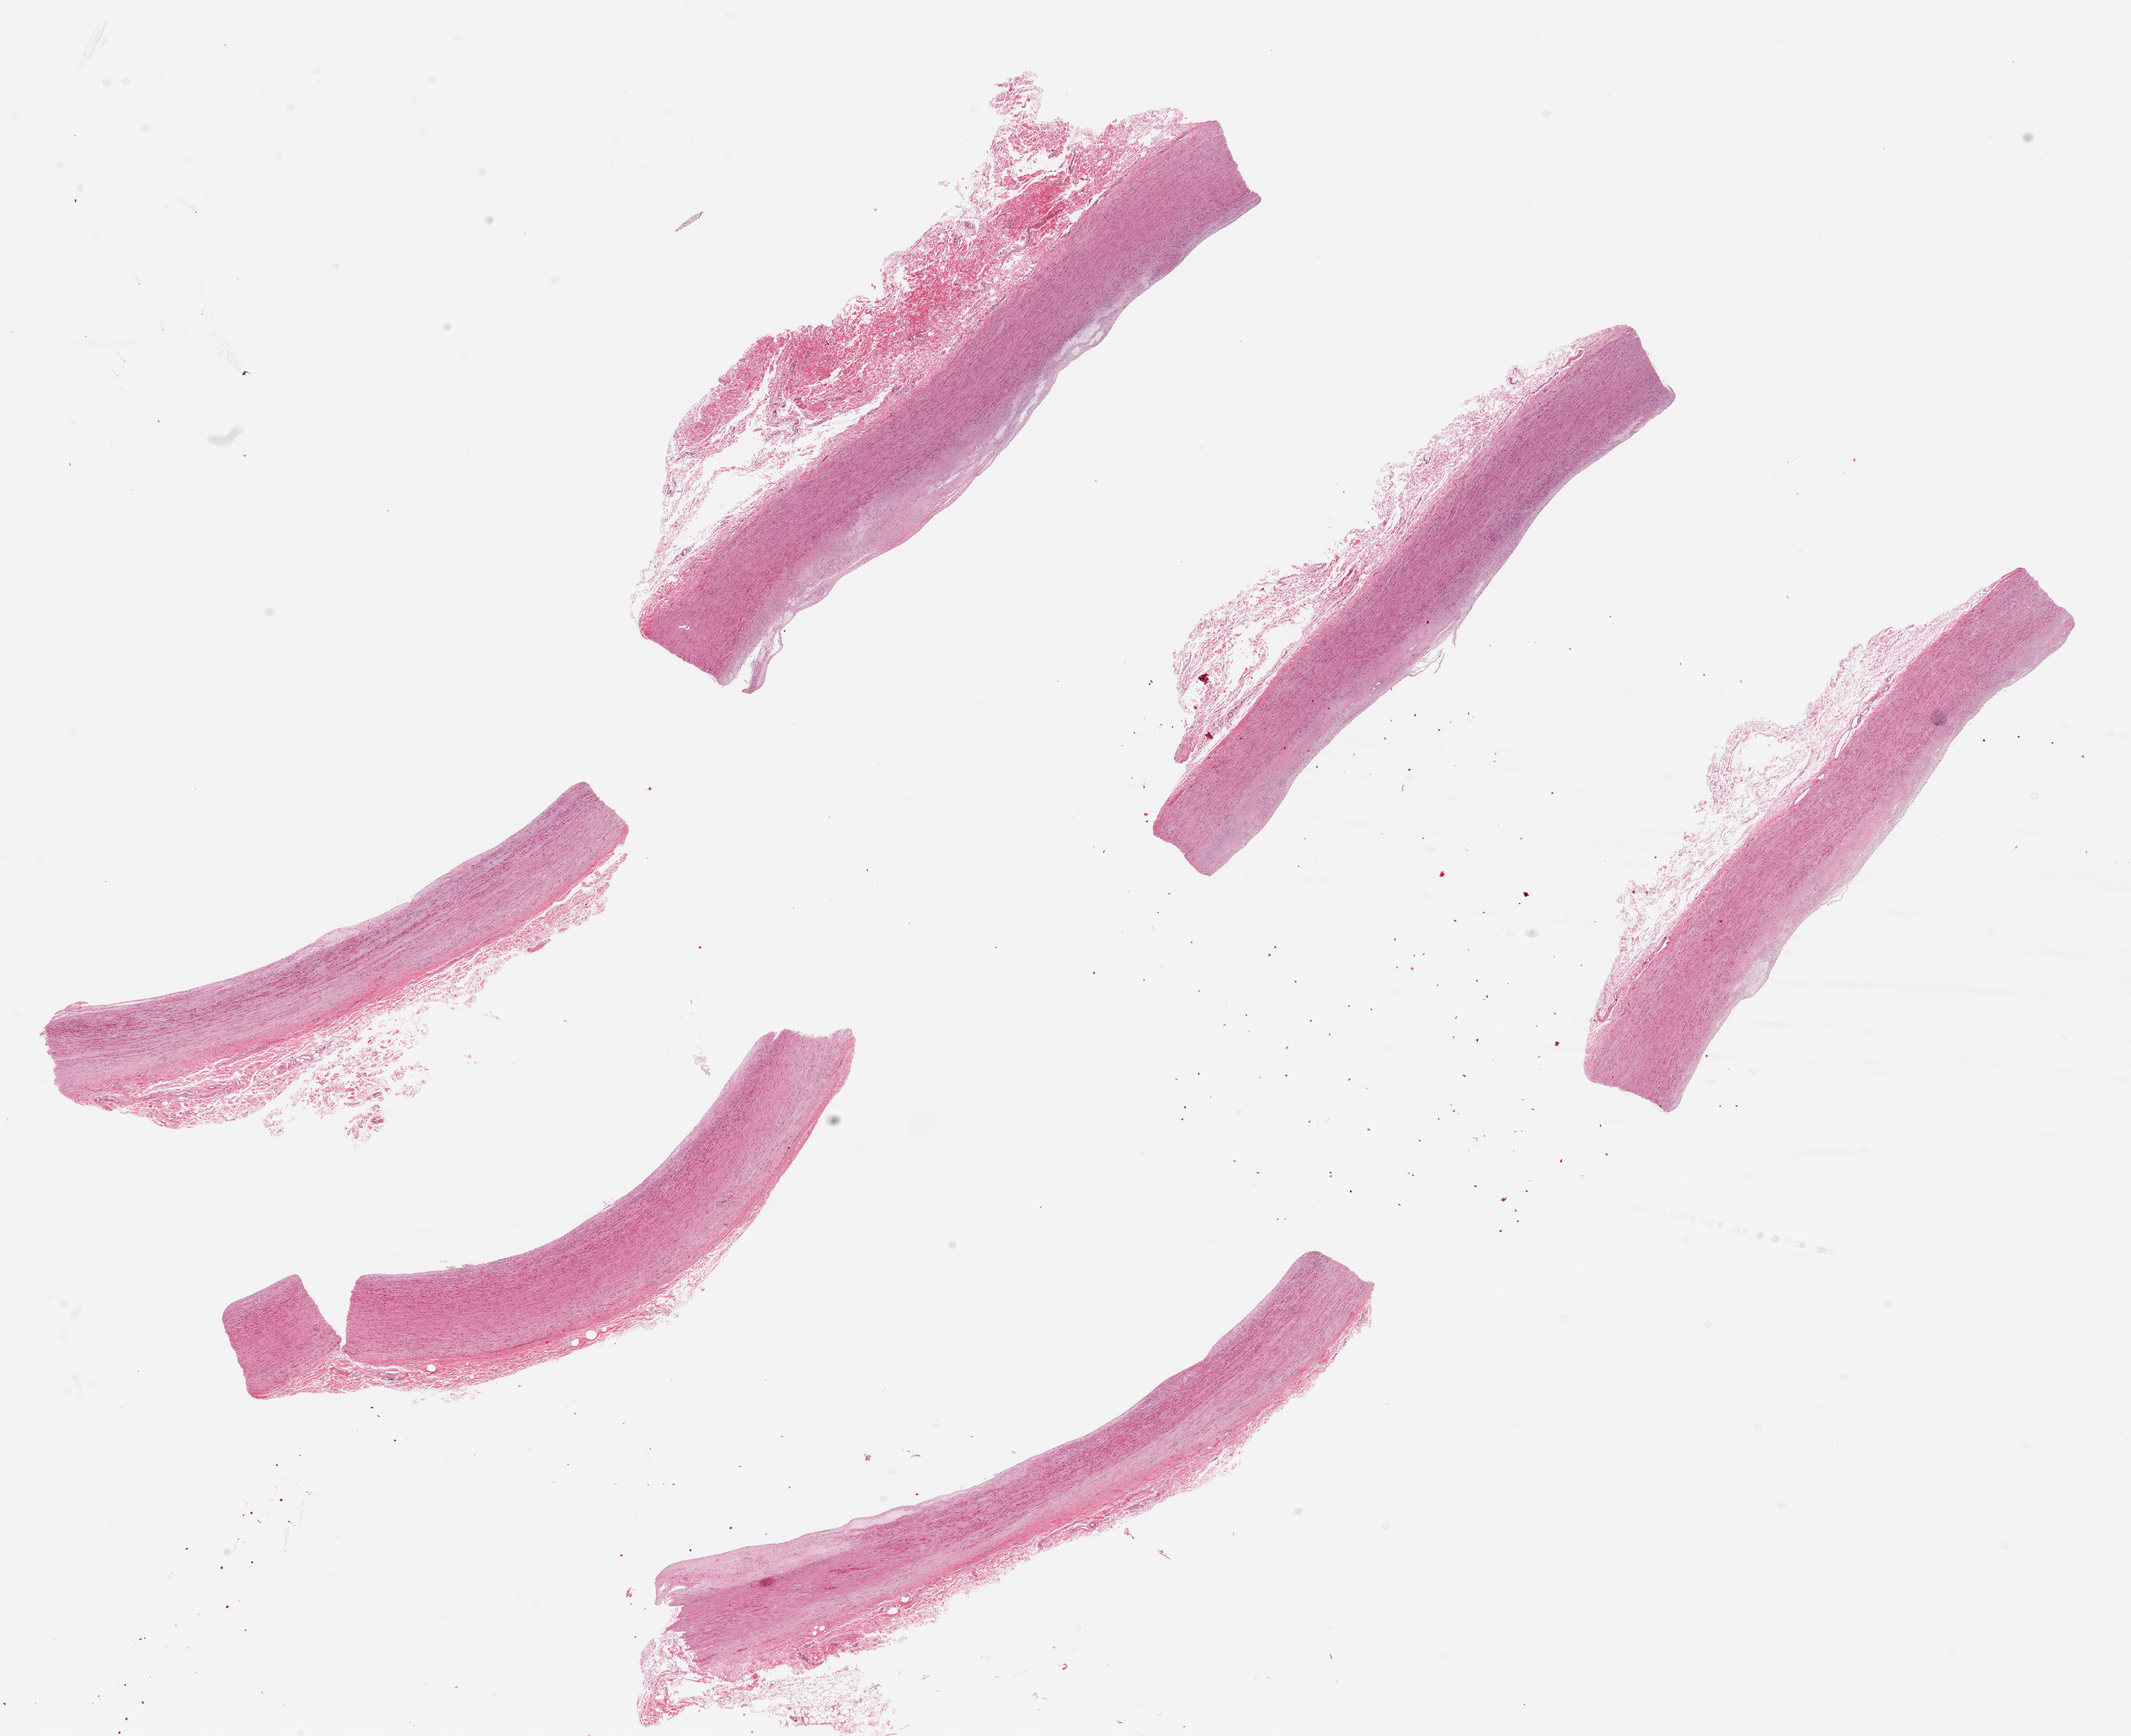
Whole-slide image, haematoxylin and eosin stain — shown as a low-resolution overview of the whole scanned area (about 25.6 x 20.8 mm, from a 20x scan). PAXgene-fixed, paraffin-embedded tissue. Sampled site (target tissue): aorta. Tissue donor sample. Donor sex: male.
Review note (as recorded): 6 pieces, ~ 9x1.2mm.